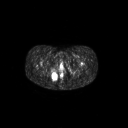
FDG PET of an extremity soft-tissue mass (from a PET/CT study), one axial slice. 128 × 128 image matrix. Female patient, age 17 years. Case-level facts recorded for this patient, not image findings: histological type: epithelioid sarcoma; grade: intermediate; site of the primary tumour: right buttock.
Annotated regions visible in this slice (expert contour drawn on MRI and transferred to this co-registered scan by the dataset authors):
- gross tumour volume including surrounding oedema: bounding box (x1, y1, x2, y2) in pixels: (49, 71, 59, 82)
- gross tumour volume (mass): (50, 72, 57, 81)